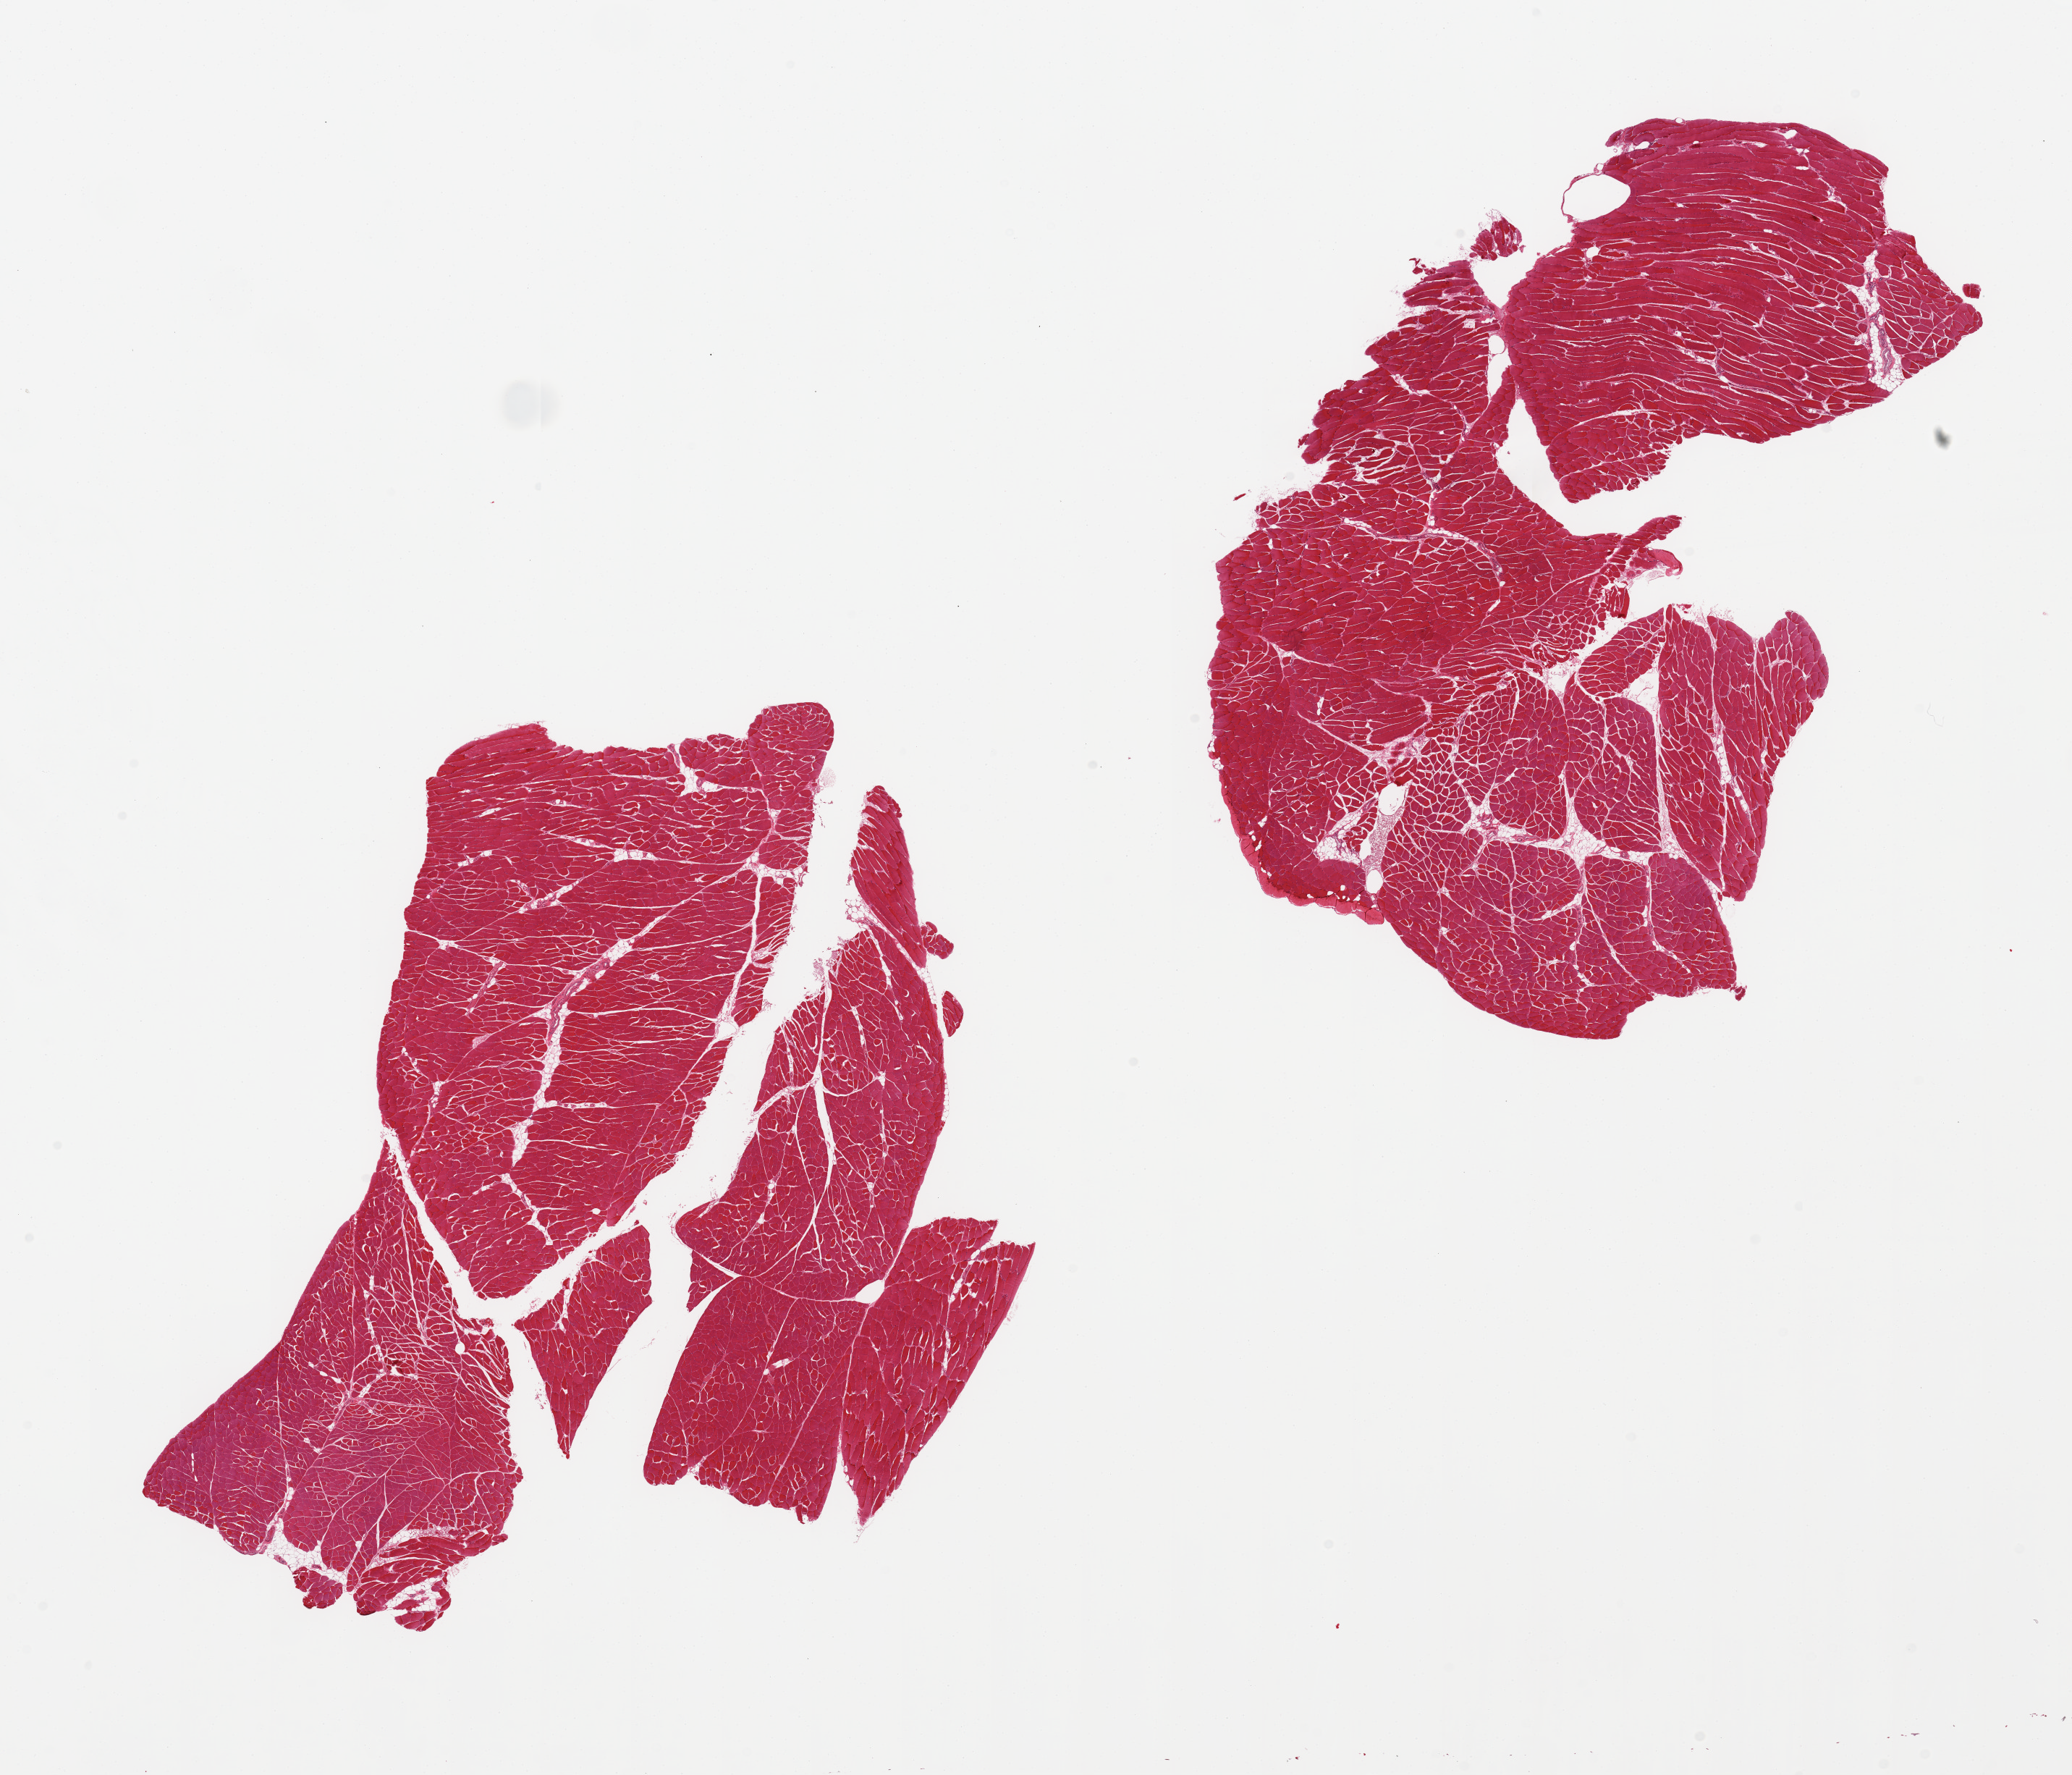
Whole-slide image, hematoxylin and eosin (H&E) stain — shown as a low-resolution overview of the whole scanned area (about 22.6 x 19.4 mm, acquisition: 20x scan), PAXgene-fixed paraffin-embedded (PFPE) section, sampled site (target tissue): skeletal muscle, donor tissue sample. Male donor.
Review note (as recorded): 2 pieces; 1% internal fat.